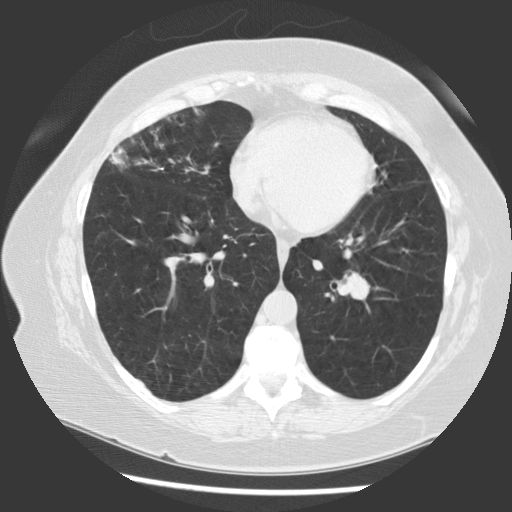
Axial slice from a low-dose chest CT screening exam; baseline screening round; lung window (W 1500 / L -600 HU); 2.5 mm slice thickness; 120 kVp; slice 54 of 130 in the series. Female participant, aged 58 years at enrolment. Former smoker at enrolment.
• Expert-annotated lung lesion, bounding box (x1, y1, x2, y2) in pixels: (328, 259, 387, 325).
• Screening reader's record for this exam (one nodule recorded; not confirmed to be the boxed lesion): non-calcified nodule or mass ≥4 mm, left lower lobe, 22 × 15 mm, smooth margins, soft tissue attenuation.
• Later outcome: lung cancer diagnosed 108 days after this screen — carcinoma, NOS, left hilum, stage IA (AJCC 6th edition), 28 mm at pathology.